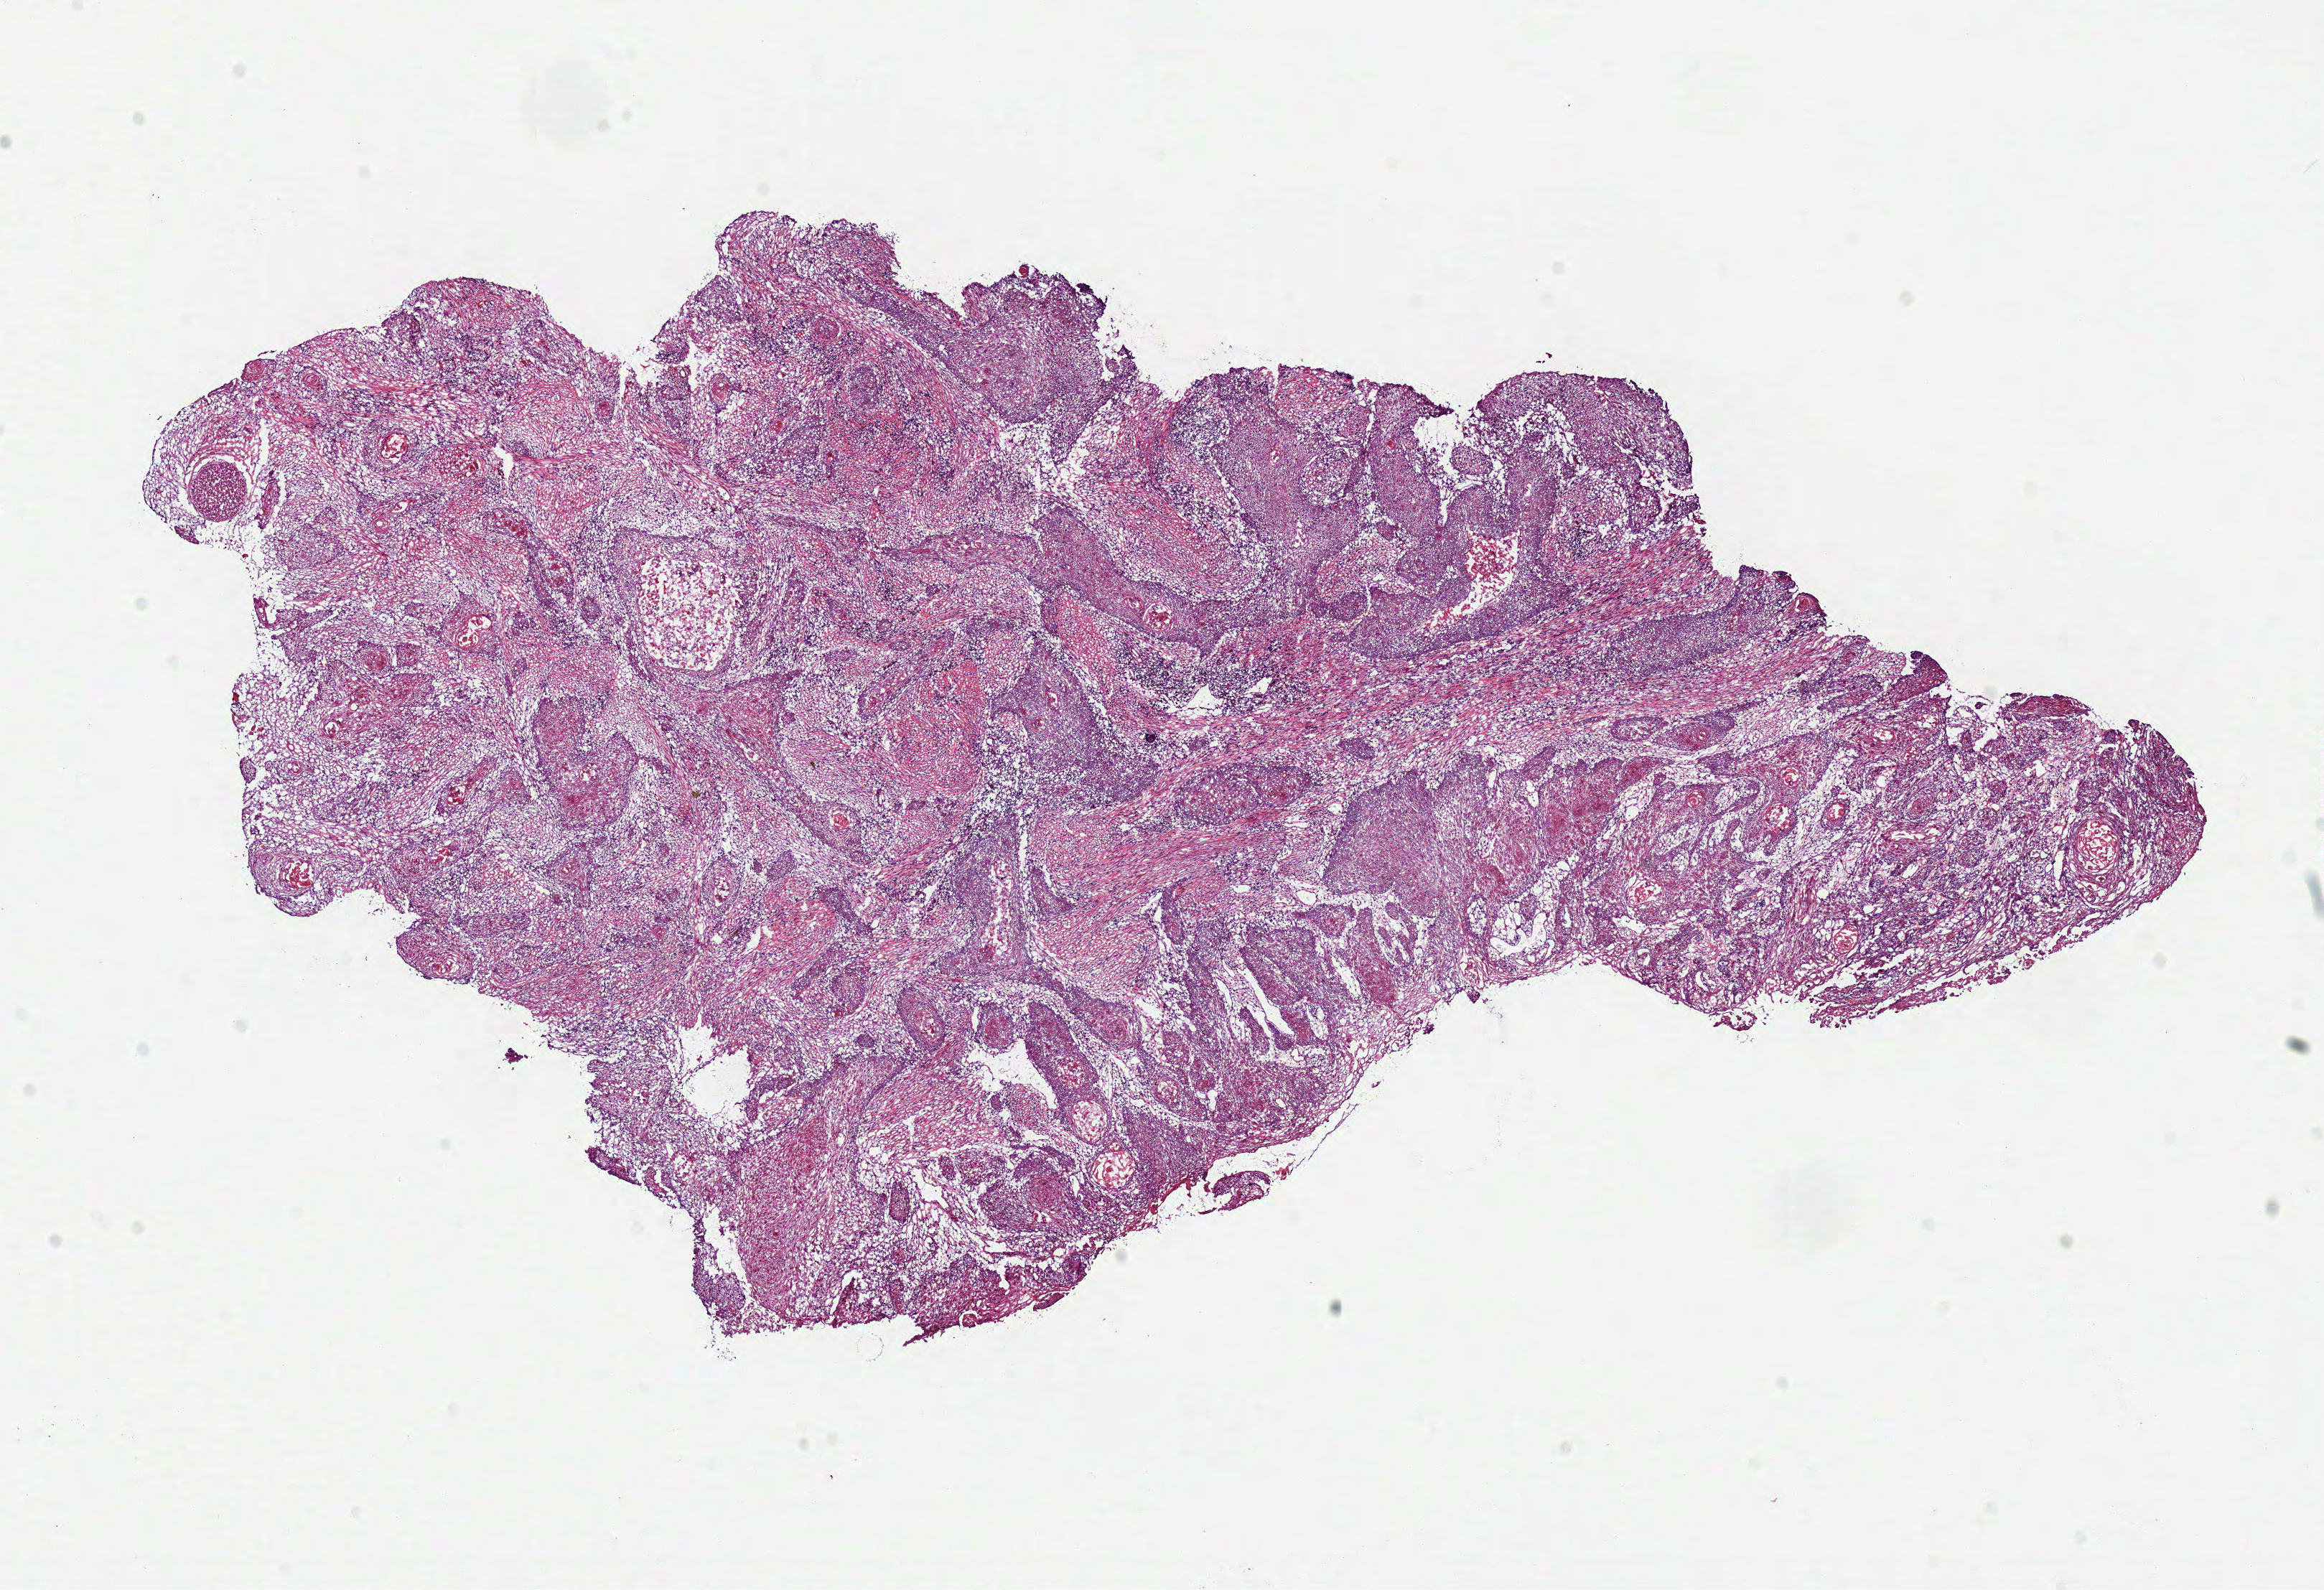
H&E-stained whole-slide image, whole scanned area (about 12.7 x 8.7 mm) shown as a low-resolution overview, frozen section from the top of the tissue portion, primary tumour sample from the head and neck. Patient: male, age at initial diagnosis 73 years. Slide review estimates, as recorded: tumour cells 80%, tumour nuclei 75%.
Diagnosis: Squamous cell carcinoma, NOS (tongue, NOS).